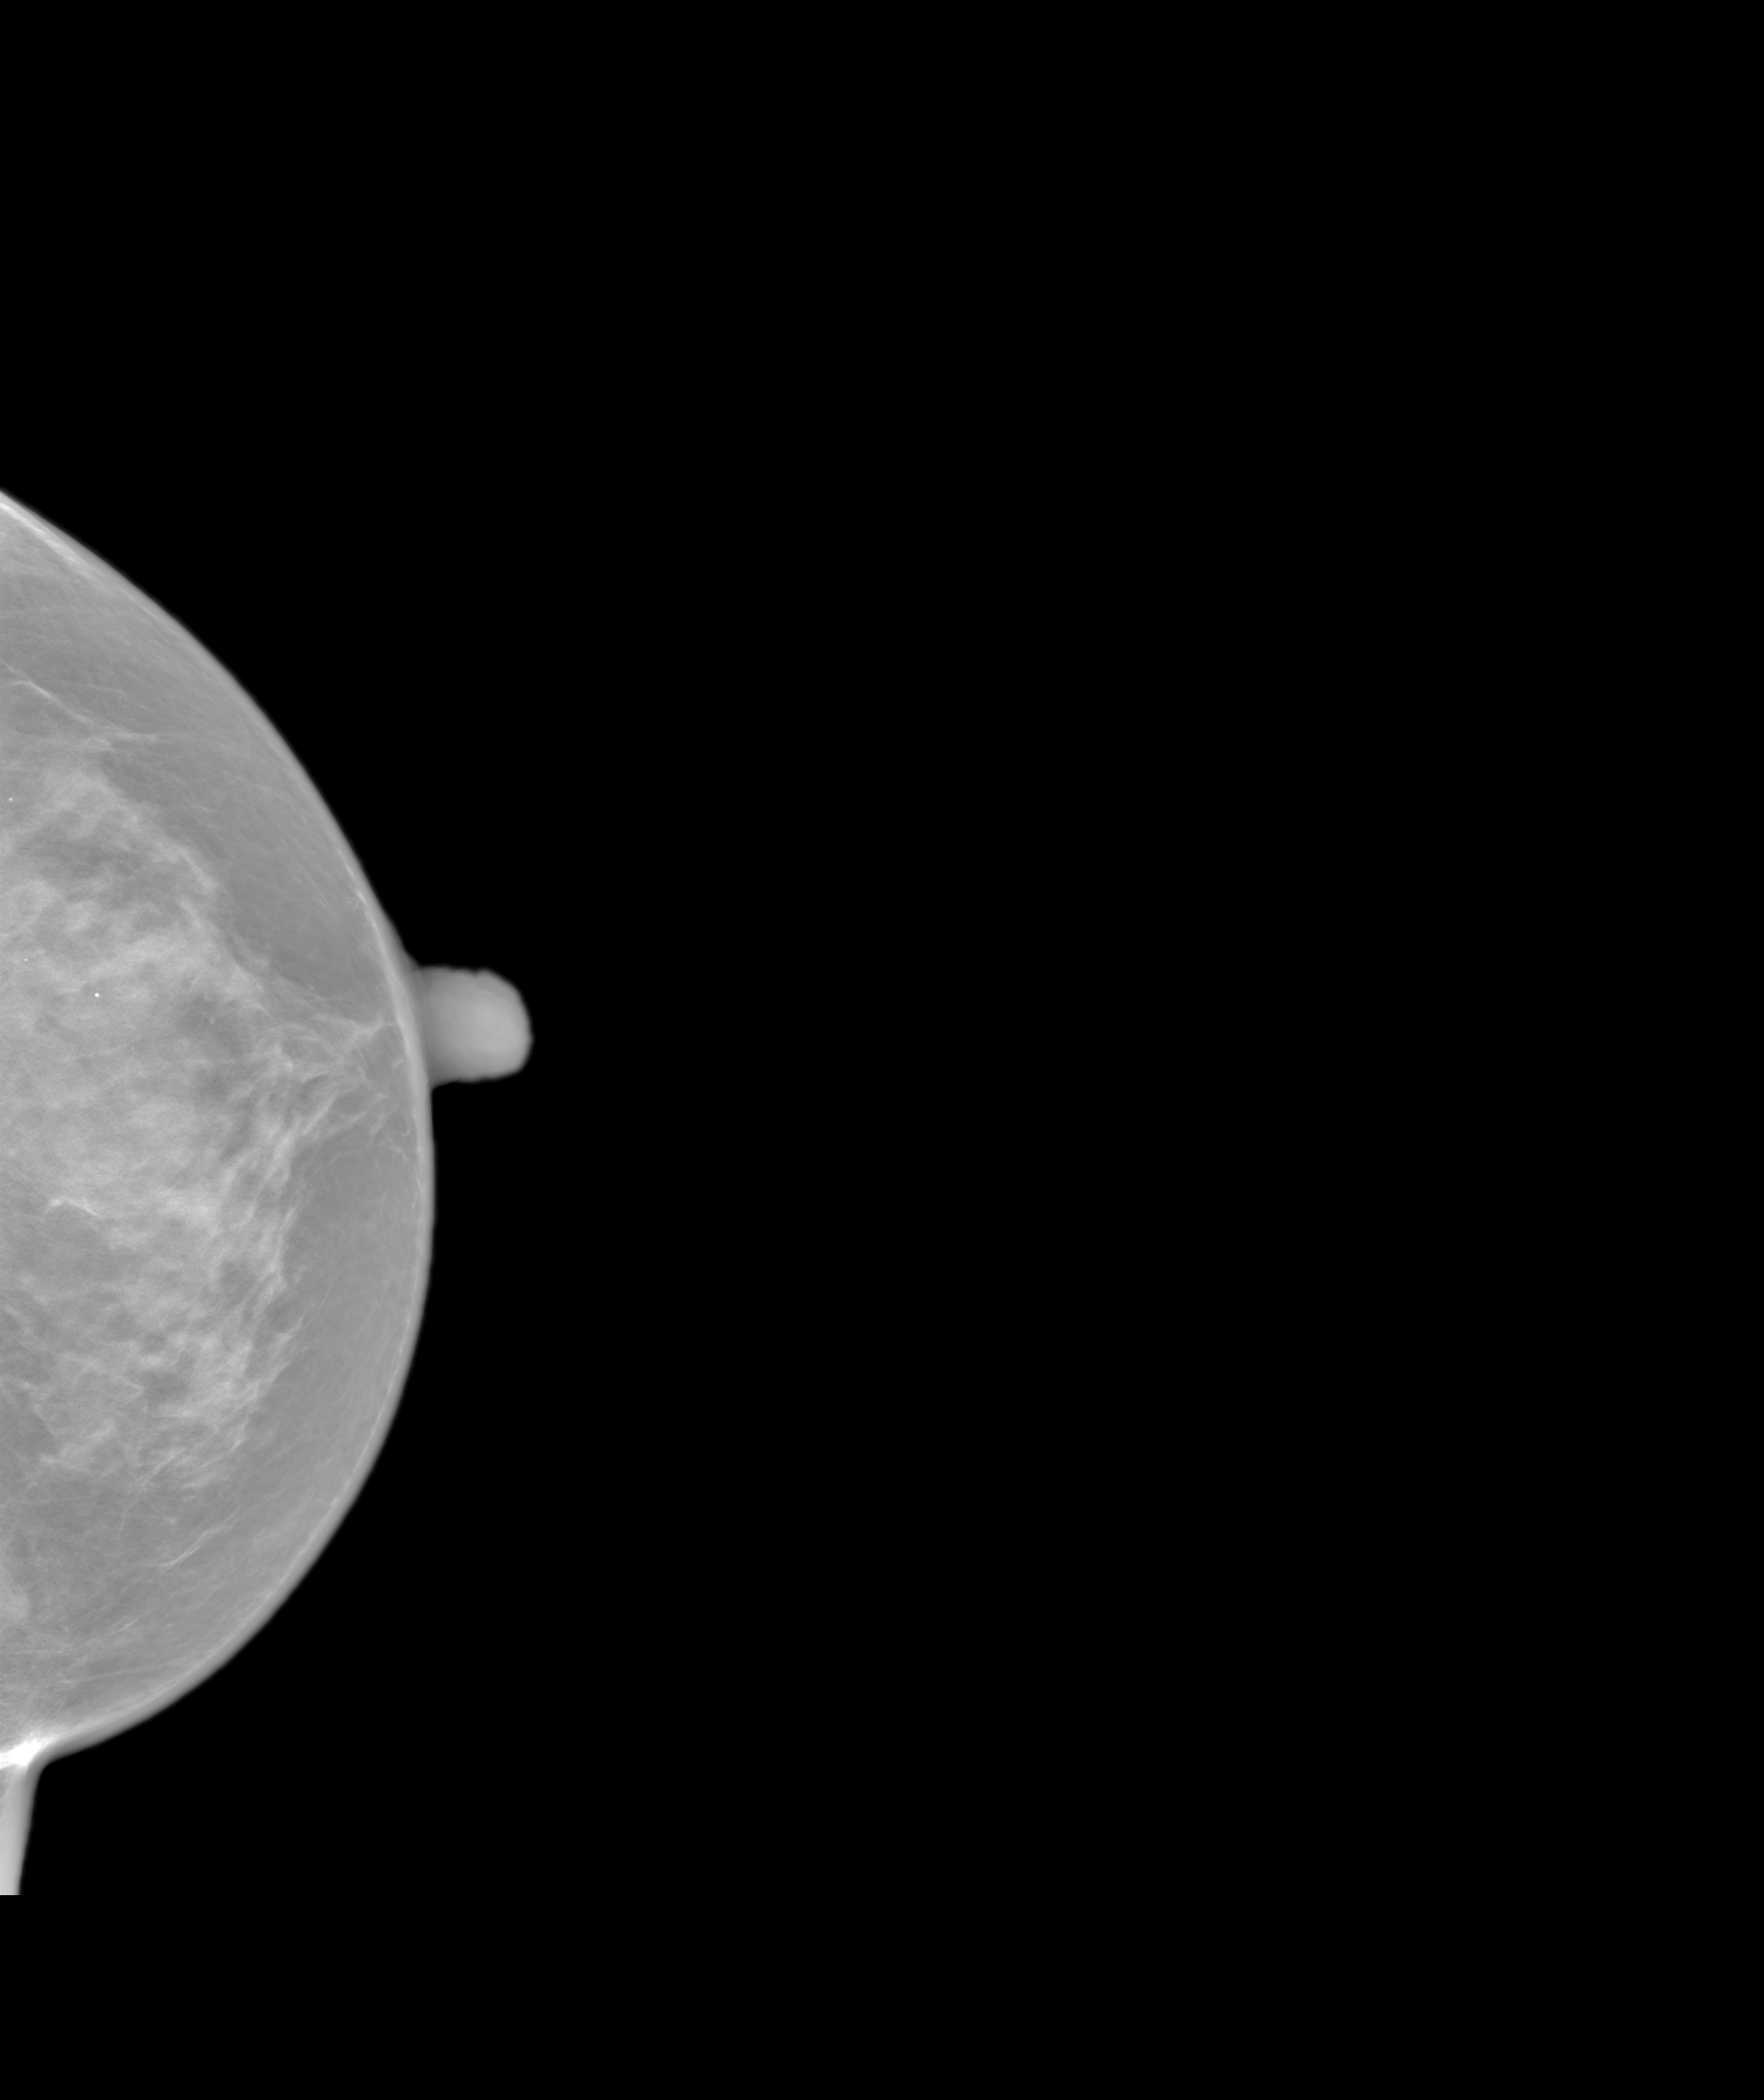
Annual screening mammography examination, system: SenoIris_1SP1.2(425).
Image type: synthesized 2-D view from tomosynthesis. Breast: left. Projection: cranio-caudal projection.